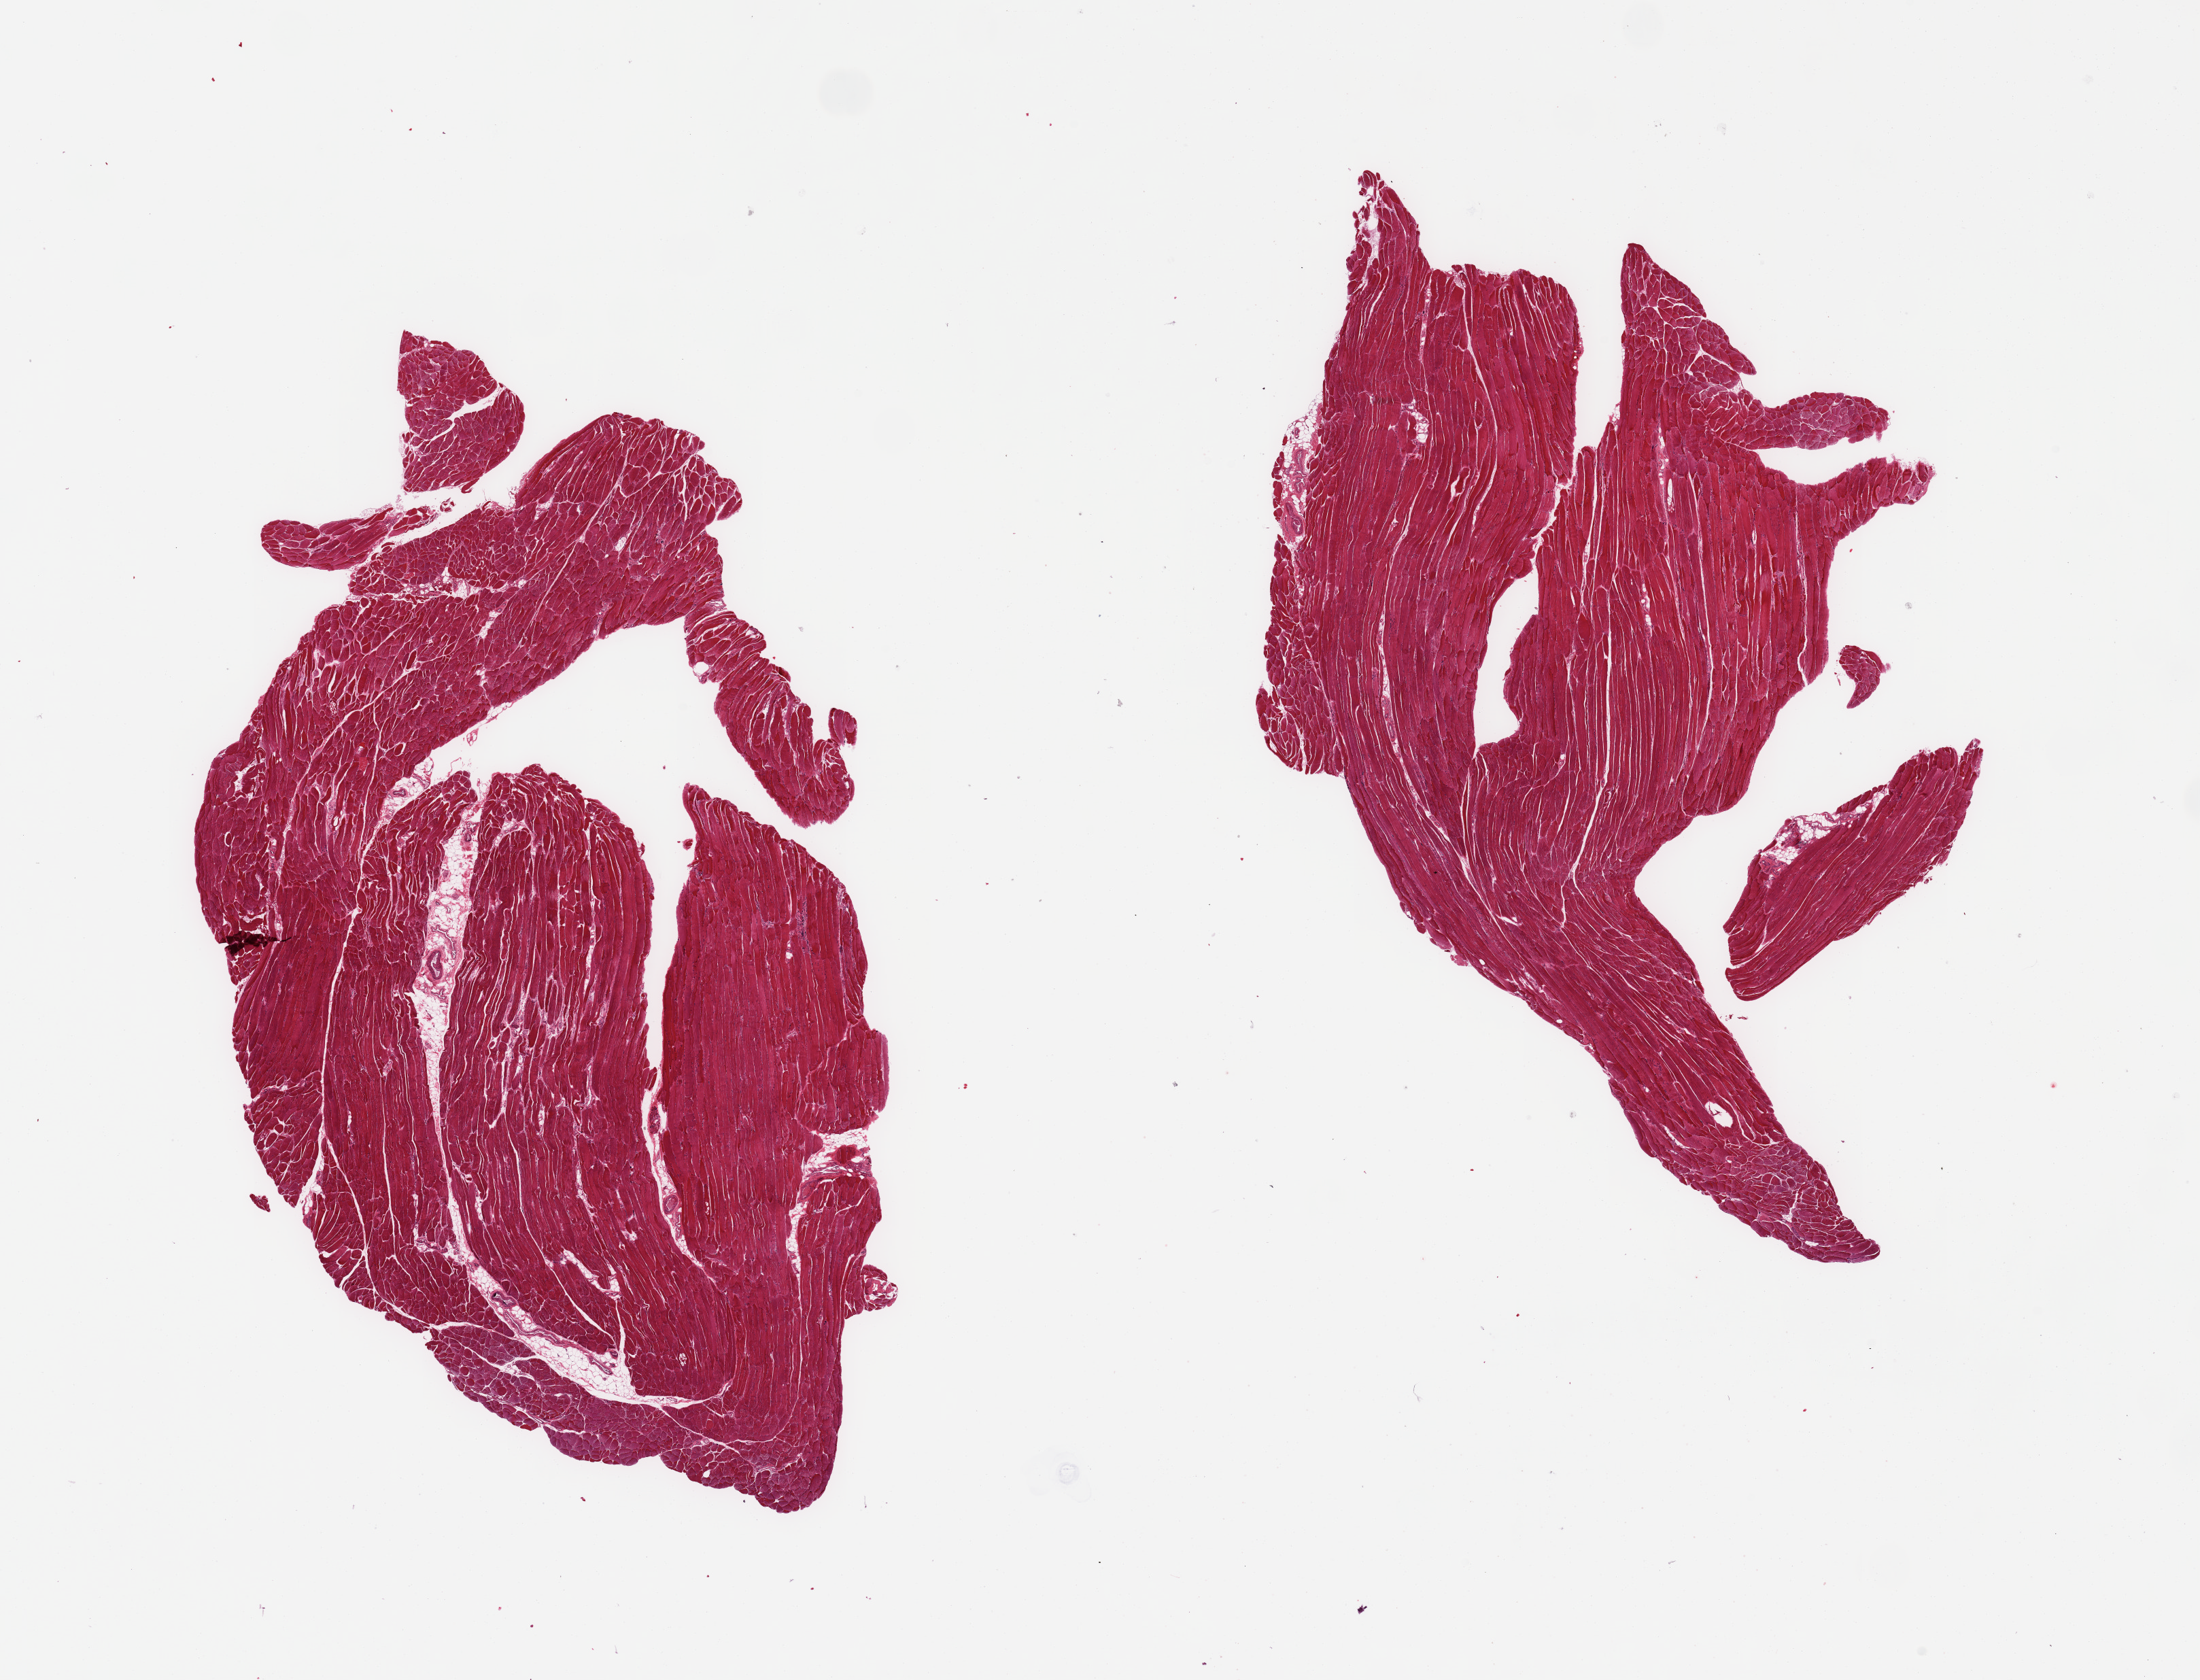
Digitized haematoxylin and eosin-stained section, low-resolution overview of the scanned area, about 25.6 x 19.5 mm (slide scanned at 20x), PAXgene-fixed paraffin-embedded (PFPE) section, section of skeletal muscle (target tissue), tissue donor sample. Donor: female.
- review note (as recorded): 2 pieces; <5% internal fat